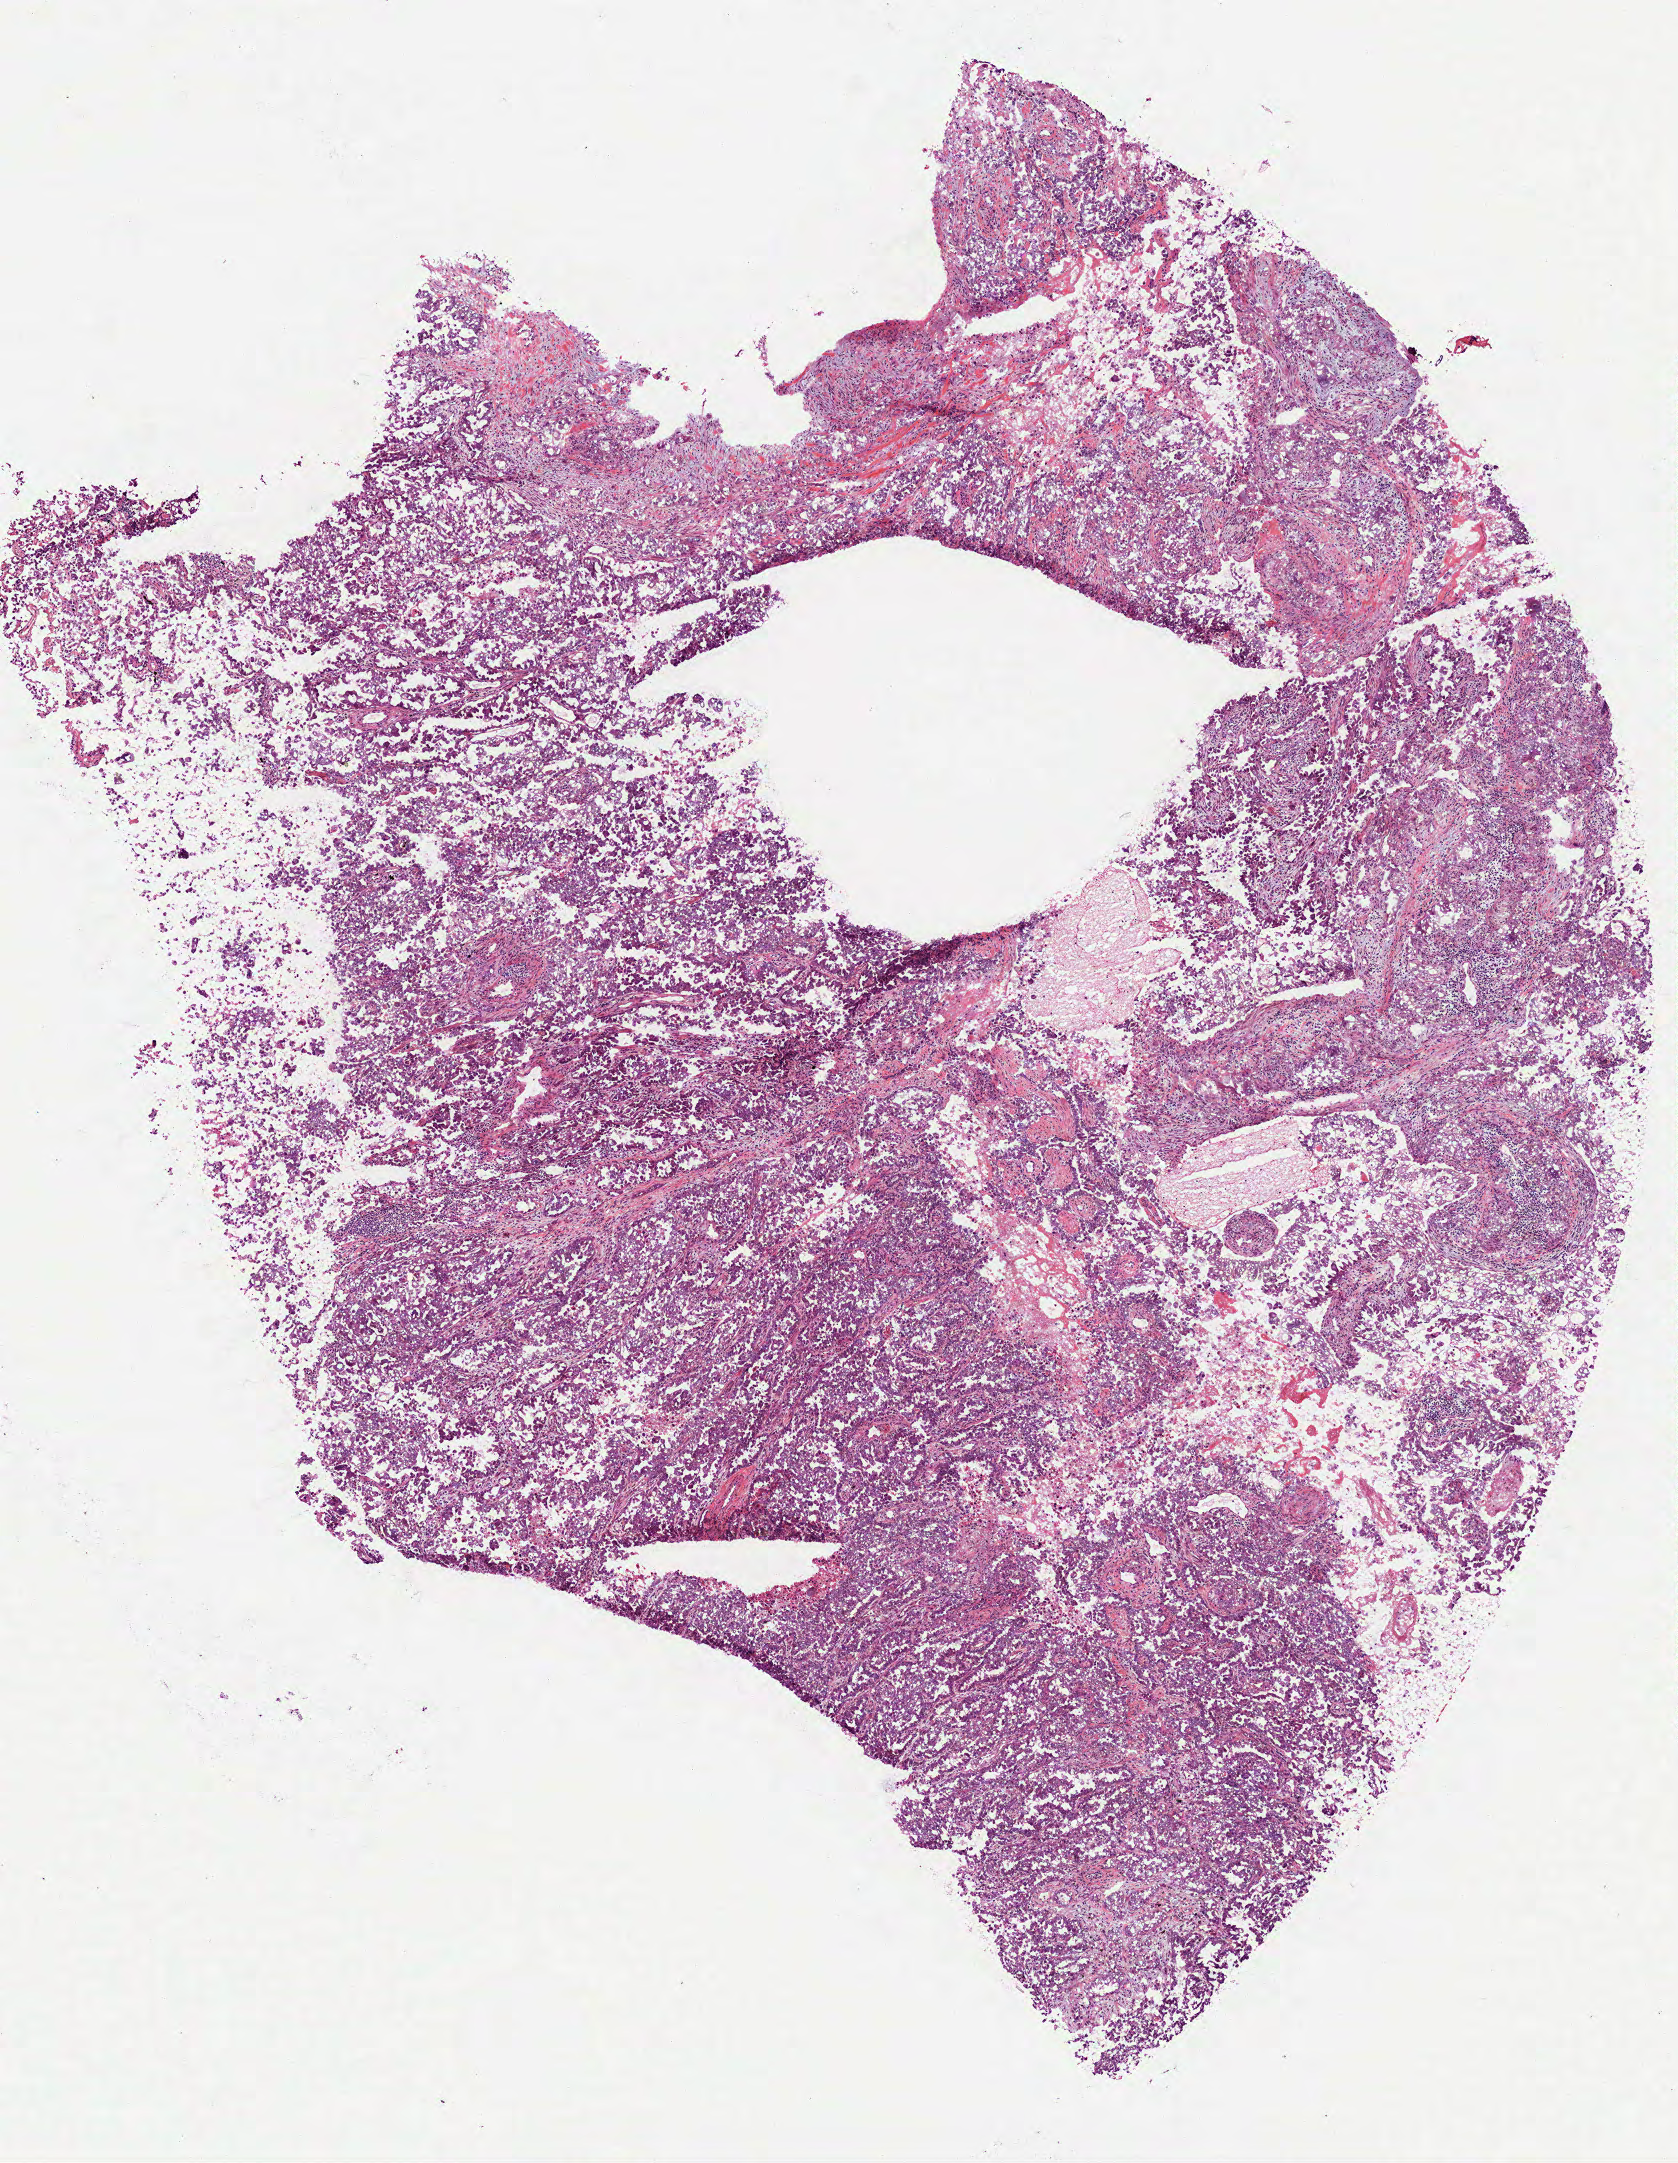
Whole-slide histology image, H&E, shown as a low-resolution overview of the whole scanned area (about 6.8 x 8.7 mm); frozen section from the bottom of the tissue portion; sample: primary tumour, lung. Female, age 52 years at initial diagnosis. Pathologist review of this section (percent, as recorded): tumour cells 75%, tumour nuclei 75%, normal cells 0%, stromal cells 10%, necrosis 15%.
* diagnosis: Adenocarcinoma, NOS
* AJCC pathologic stage: IV (6th edition)
* laterality: right